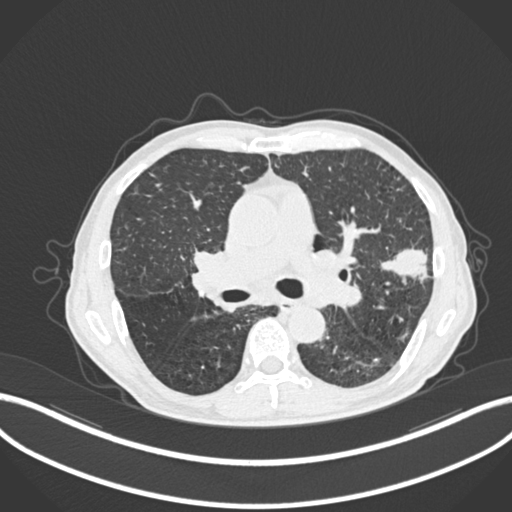
Chest CT, one axial slice. Slice 144 of 287 in the series (ordered by position). Reconstruction kernel B30f. 120 kVp. Lung window (W 1500 / L -600 HU). 512 × 512 image matrix, field of view 400 × 400 mm. Patient: male, 74 years. Case-level facts recorded for this patient, not image findings: clinical TNM (as recorded): T2a N1 M0.
Structures marked on this image (bounding box drawn by a radiologist):
- lung tumour (recorded histology: adenocarcinoma): bounding box (x1, y1, x2, y2) in pixels: (375, 243, 433, 285)